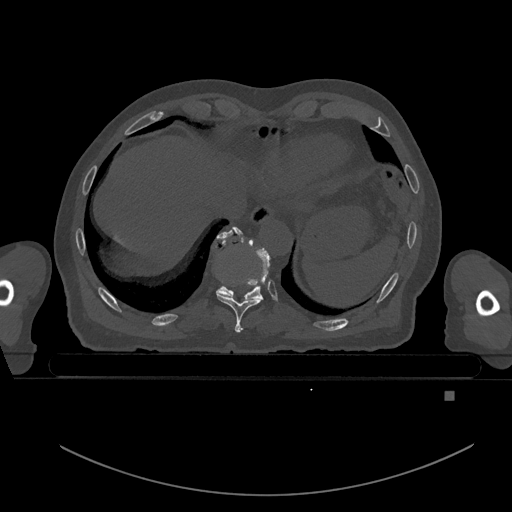
CT including the spine, one axial slice; position 123 of 969 along the scan axis; bone window (W 1800 / L 400 HU); 0.5 mm slice thickness; 512 × 512 image matrix. Male patient, age 82 years. From the clinical record (not read from this slice): primary cancer: prostate; vertebrae with lytic lesions (as recorded): T11, T9, T8, T2.
Structures marked on this image (semi-automatic segmentation, software-assisted and operator-edited):
- T10 vertebra: bounding box <218,226,270,299> (left, top, right, bottom; pixels)
- T9 vertebra: <216,230,263,332>